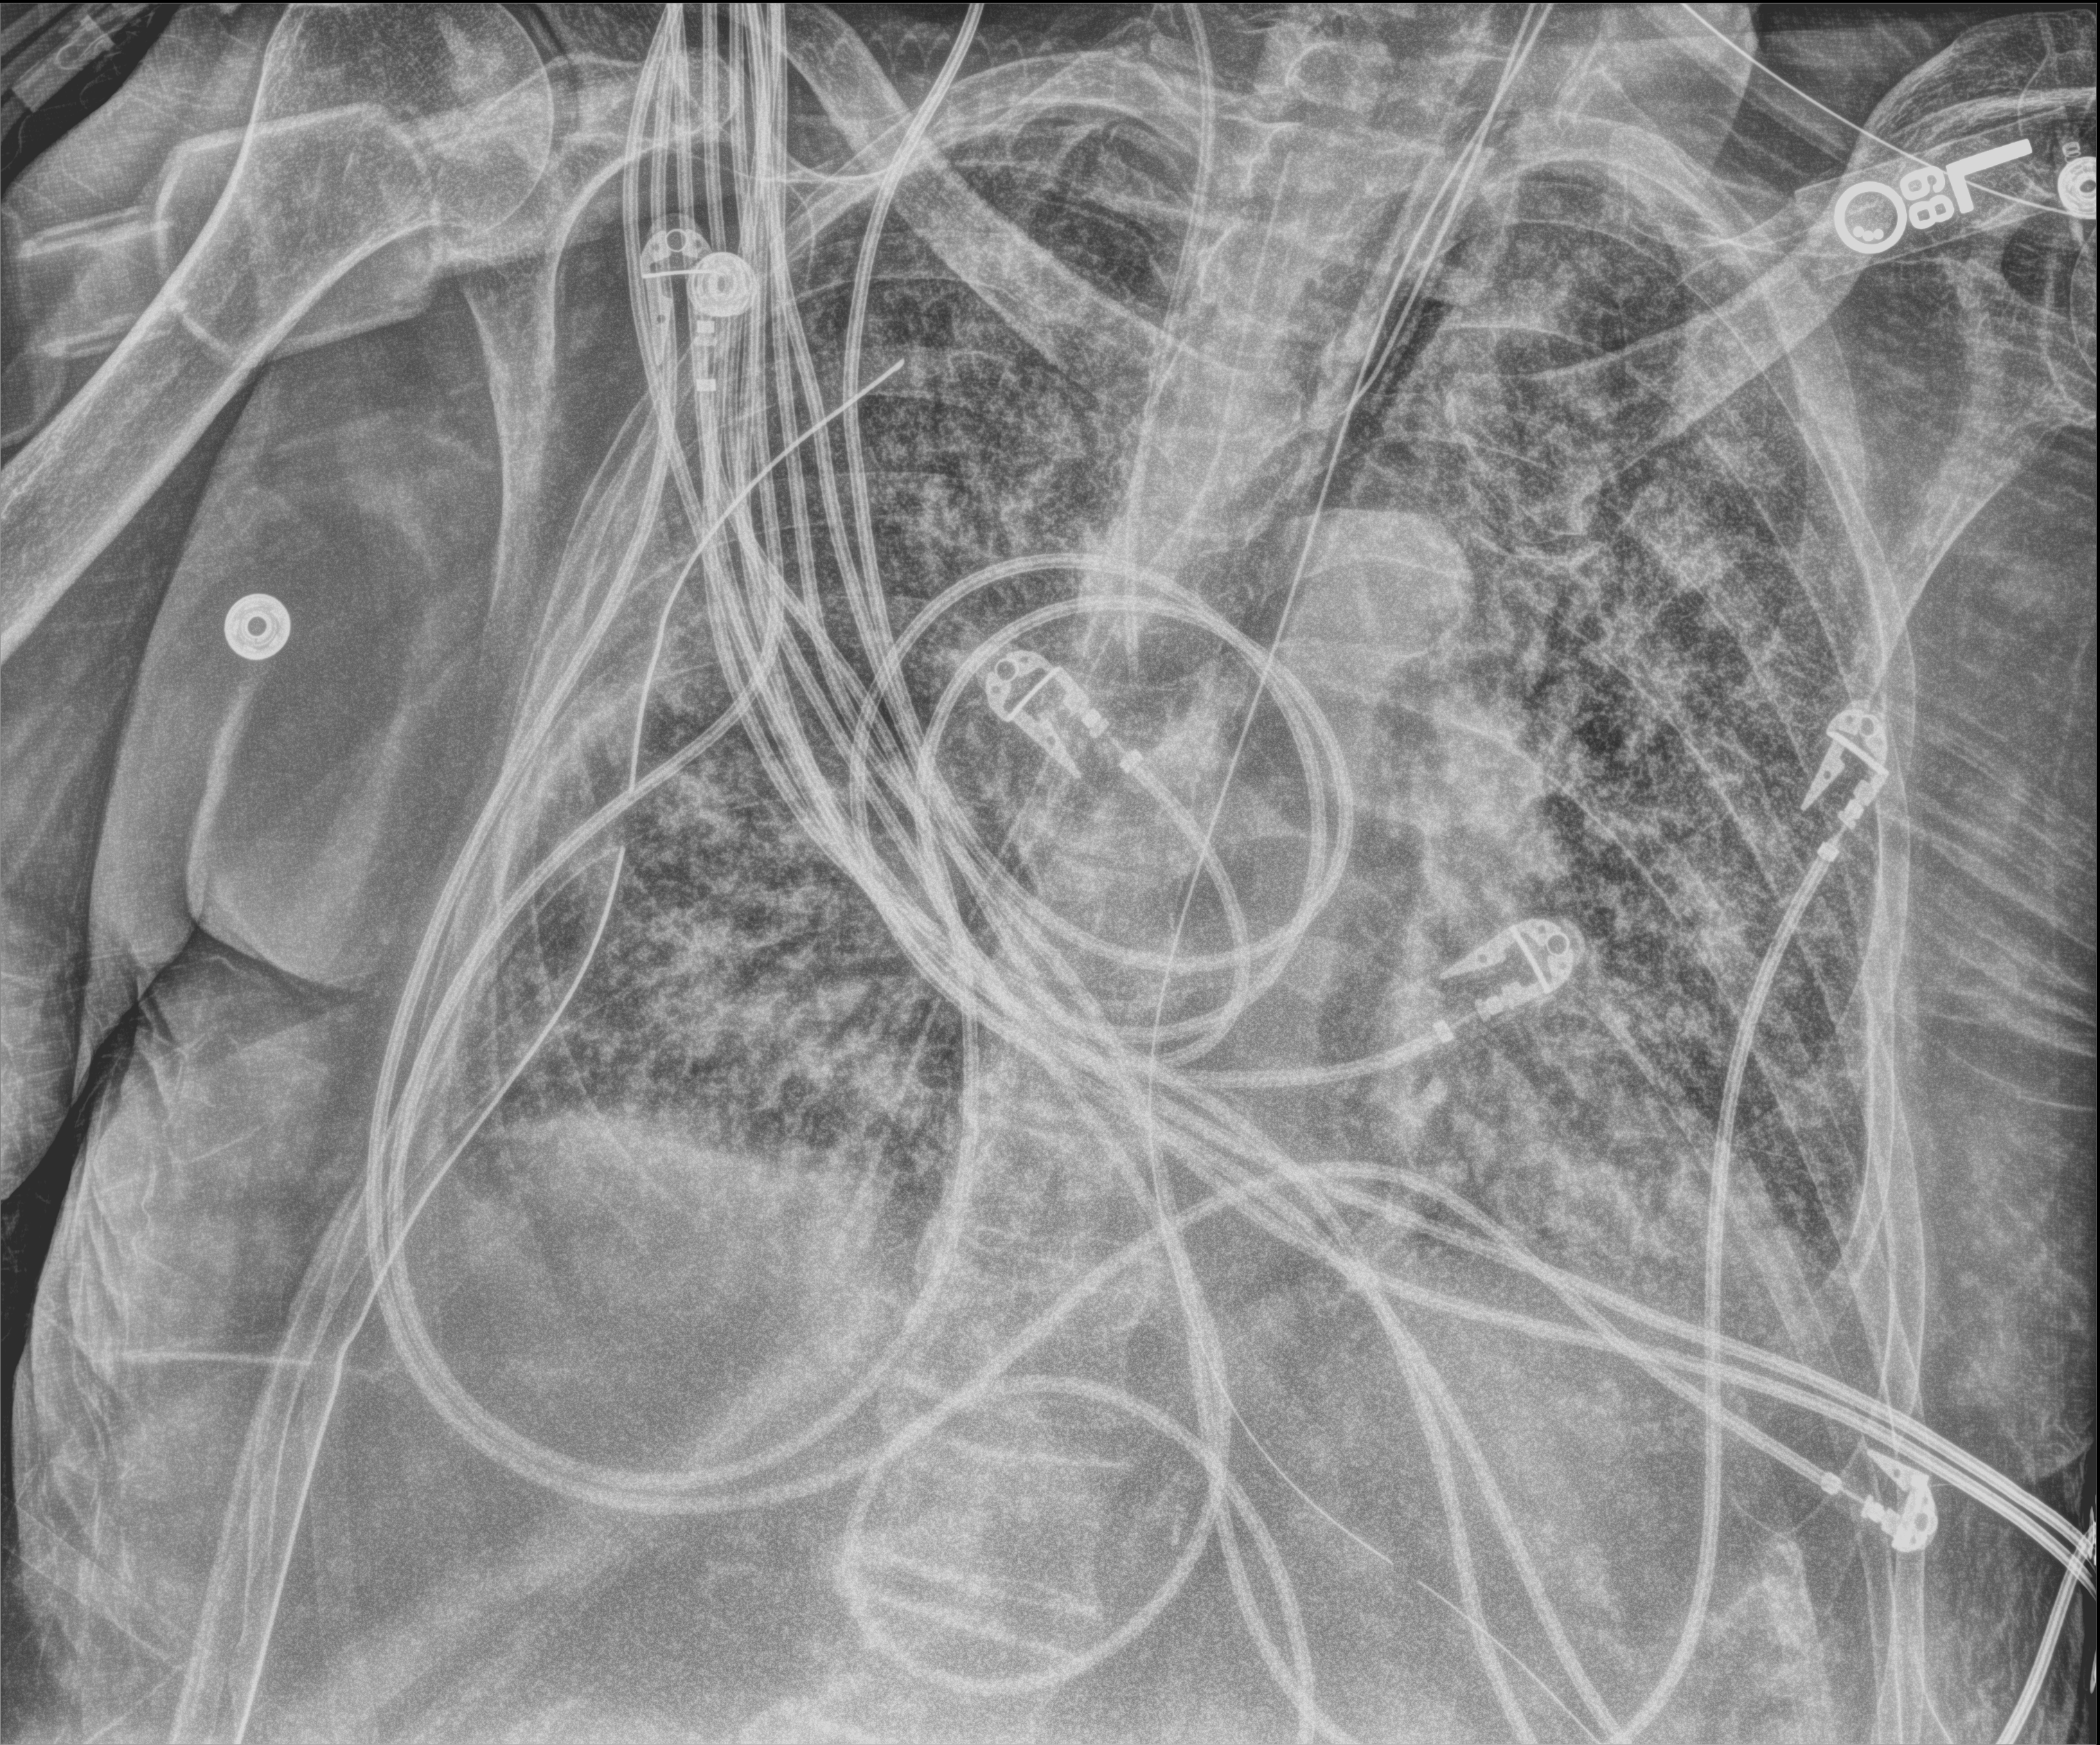
Chest X-ray (portable). Male patient hospitalised with COVID-19, age 75–90 years.
Hospital-stay facts (about this admission, not read from this image; timing relative to this image not recorded): chronic kidney disease (admission record): no; length of hospital stay: 47 days; admitted to intensive care during this hospital stay: yes.